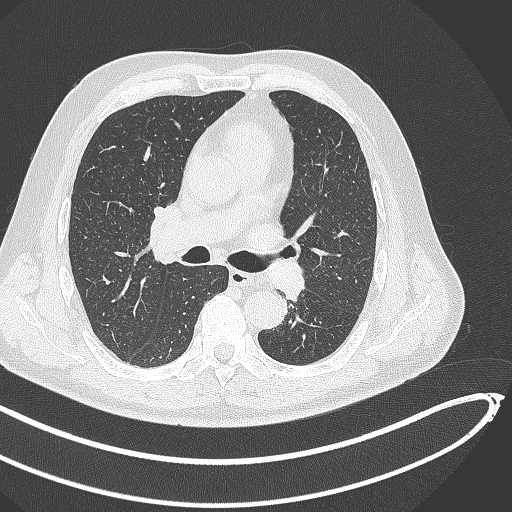
Chest CT, one axial slice. Position 275 of 468 along the scan axis. Reconstruction kernel B70f. 120 kVp. Lung window (W 1500 / L -600 HU). 512 × 512 image matrix, field of view 400 × 400 mm. Patient: male, 64 years. Case-level facts recorded for this patient, not image findings: clinical TNM (as recorded): T1c N0 M0.
Structures marked on this image (rectangle marked by the reading radiologist):
- lung tumour (recorded histology: squamous cell carcinoma): bounding box (x1, y1, x2, y2) in pixels: (265, 255, 308, 302)